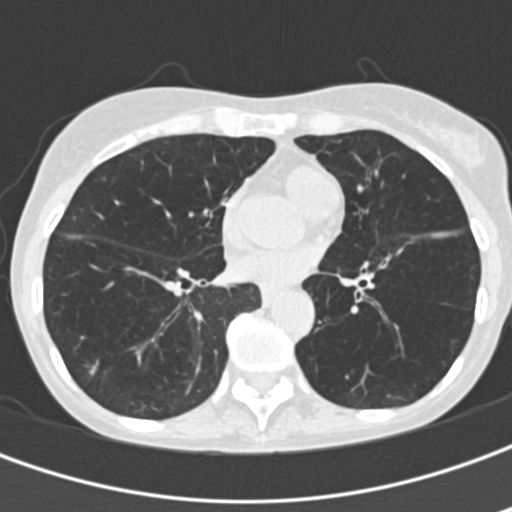
Axial slice from a low-dose chest CT screening exam. Second screening round (one year after baseline). Lung window (W 1500 / L -600 HU). Standard (soft-tissue) reconstruction kernel (B30f). Slice 103 of 201 in the series. 512 × 512 image matrix, field of view 280 × 280 mm. Female participant, aged 68 years at enrolment. Former smoker at enrolment.
Expert reader's lesion annotation, bounding box <75,352,113,394> (left, top, right, bottom; pixels). Screening reader's record for this exam (one nodule recorded; not confirmed to be the boxed lesion): non-calcified nodule or mass ≥4 mm, right lower lobe, 9 × 7 mm, spiculated (stellate) margins, soft tissue attenuation, pre-existing on the prior screen: yes; interval growth: yes. Official screen result: positive, other. Lung cancer was diagnosed 659 days after this screen: squamous cell carcinoma, NOS, right lower lobe, stage IA (AJCC 6th edition).